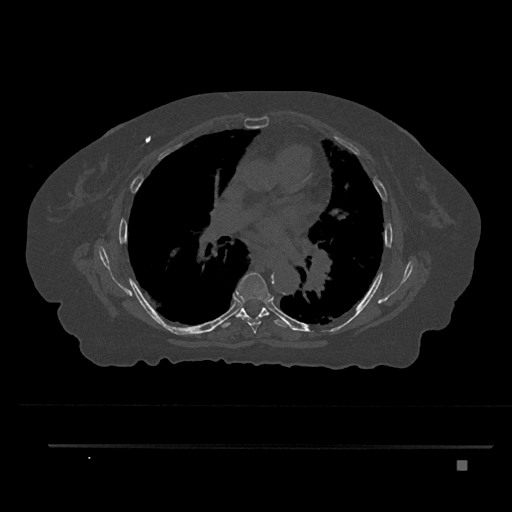
CT including the spine, one axial slice; slice 509 of 797 in the series (ordered by position); reconstruction kernel Br40s/3; bone window (W 1800 / L 400 HU); 0.5 mm slice thickness; 512 × 512 image matrix, field of view 437 × 437 mm. Female patient, age 76 years. From the clinical record (not read from this slice): primary cancer: lung; vertebrae with lytic lesions (as recorded): T11, L3.
Outlined on this slice (semi-automatically segmented with operator editing):
- T6 vertebra: bounding box [x1, y1, x2, y2] px = [234, 272, 271, 333]
- T7 vertebra: [221, 307, 289, 328]